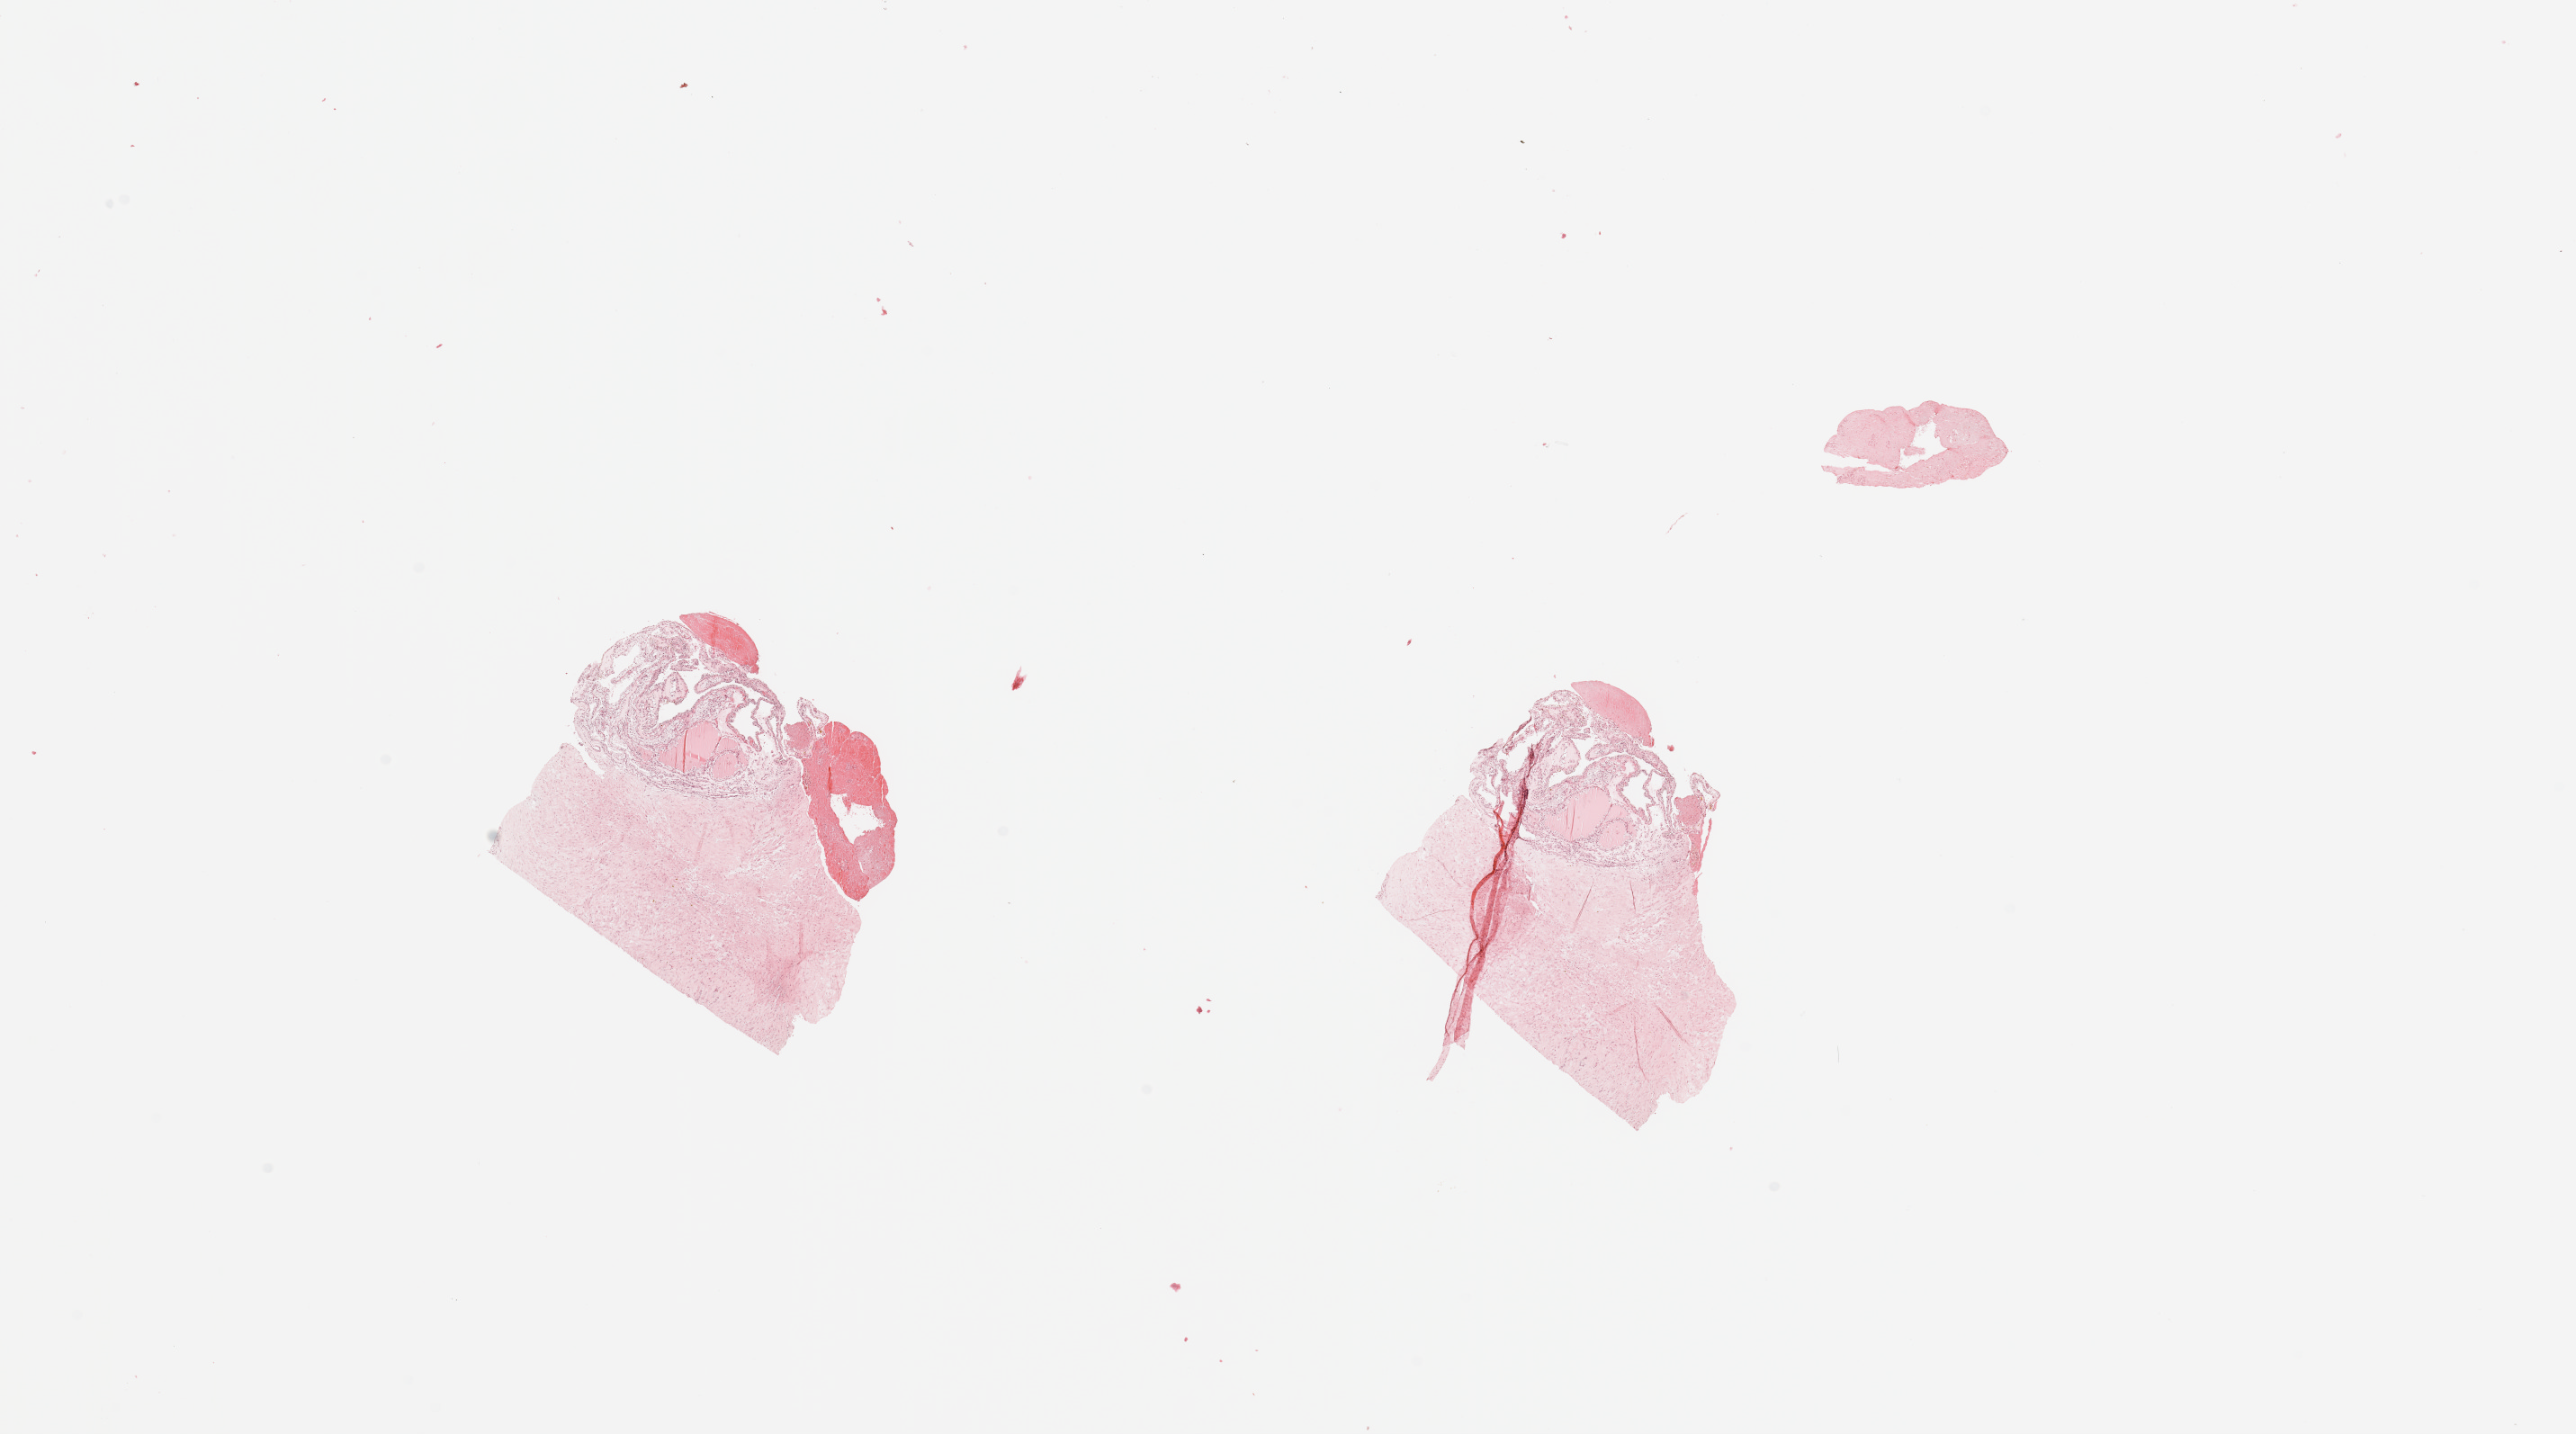
Whole-slide histology image, H&E, low-resolution overview of the scanned area, about 22.6 x 12.6 mm (from a 20x scan). Tumour tissue sample, sampled site: kidney. 61-year-old male patient. Composition of this section per pathologist review: tumour nuclei 80%, necrosis 0%.
Histologic diagnosis: Renal cell carcinoma, NOS.